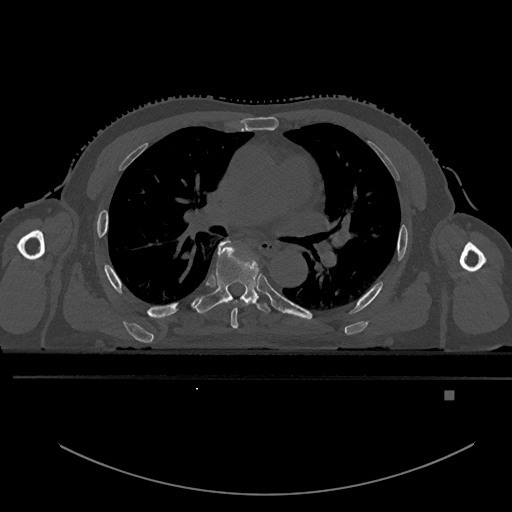
CT including the spine, one axial slice. Slice 325 of 969 in the series (ordered by position). Bone window (W 1800 / L 400 HU). 0.5 mm slice thickness. 512 × 512 image matrix, field of view 456 × 456 mm. Male patient, age 82 years. From the clinical record (not read from this slice): primary cancer: prostate.
Annotated regions visible in this slice (semi-automatic segmentation, software-assisted and operator-edited):
- T5 vertebra: box from (x=226, y=240) to (x=252, y=329) px
- T6 vertebra: (x=191, y=240)–(x=271, y=314)